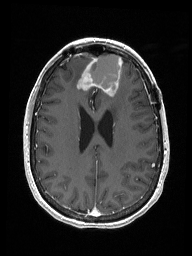
Brain MRI from a brain-tumour surgery series, one axial slice; slice 64 of 192 in the series (ordered by position); T1-weighted post-contrast; 192 × 256 image matrix, field of view 187 × 250 mm. Case-level facts recorded for this patient, not image findings: histopathology: Metastastic Carcinoma from Breast primary; tumour location: Right Frontal.
Outlined on this slice (outlined manually by an expert reader):
- previous resection cavity: bounding box [x1, y1, x2, y2] px = [89, 54, 122, 95]